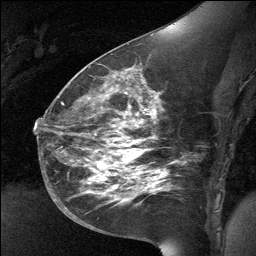
Breast MRI (dynamic contrast-enhanced), one sagittal slice; slice 36 of 64 in the series (ordered by position); dynamic contrast-enhanced study with each time point stored as its own series, time point 2 of 3 at this slice position (early post-contrast, ordered by acquisition time); 1.5 T; TE 4.8 ms, TR 27 ms; 256 × 256 image matrix. Female patient, age 39 years. From the clinical record (not read from this slice): setting: breast cancer imaged before/during neoadjuvant chemotherapy; receptor status: HER2-positive.
Structures marked on this image (semi-automatic segmentation, software-assisted and operator-edited):
- analysis volume of interest (the breast-tissue region the enhancement analysis was run in; not a lesion): box from (x=70, y=69) to (x=168, y=224) px
- tumour enhancement mask (voxels above the 90 % enhancement threshold inside the analysis volume of interest): (x=92, y=138)–(x=160, y=192)